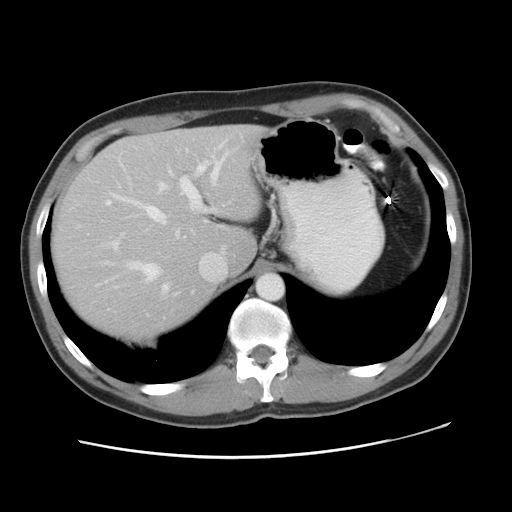
Contrast-enhanced abdominal CT, one axial slice. Position 36 of 49 along the scan axis. Intravenous contrast given. Soft-tissue window (W 400 / L 40 HU). 5 mm slice thickness. 512 × 512 image matrix, field of view 363 × 363 mm. Male patient, age 41 years. From the clinical record (not read from this slice): diagnosis: colorectal cancer liver metastases, imaged before liver resection; multiple liver metastases: yes; largest metastasis: 0.7 cm; disease in both lobes: yes.
Structures marked on this image (manually delineated by an expert):
- hepatic veins: bounding box [x1, y1, x2, y2] px = [105, 156, 226, 294]
- liver: [50, 126, 259, 339]
- planned liver remnant (the part of the liver to remain after resection): [99, 126, 259, 271]
- portal vein (with intrahepatic branches): [109, 141, 224, 249]